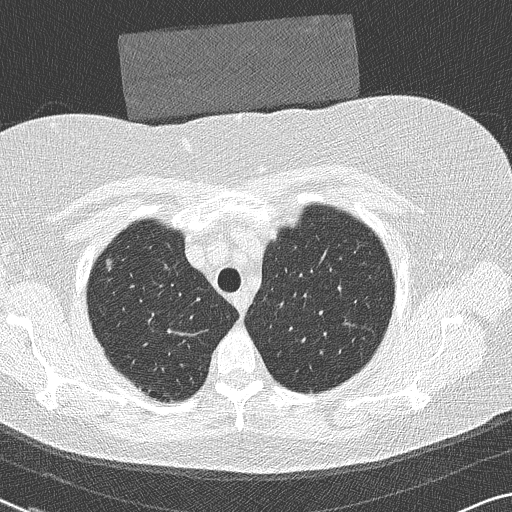
Chest CT (low-dose screening protocol), one axial image. Baseline screening round. Lung window (W 1500 / L -600 HU). 2 mm slice thickness. Lung (sharp) reconstruction kernel (B50f). 512 × 512 image matrix. Female, age 58 years at enrolment.
• Expert reader's lesion annotation, bounding box [x1, y1, x2, y2] px = [89, 244, 131, 290].
• No non-calcified nodule or mass ≥4 mm was recorded by the screening reader at this exam.